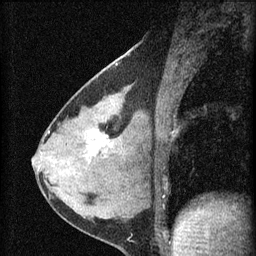
Breast MRI (dynamic contrast-enhanced), one sagittal slice; slice 28 of 60 in the series (ordered by position); dynamic contrast-enhanced series, image 2 of 4 at this slice position (ordered by acquisition); 1.5 T; TE 4.2 ms, TR 8.2 ms; 2 mm slice thickness; 256 × 256 image matrix, field of view 180 × 180 mm. Female patient, age 37 years.
Annotated regions visible in this slice (semi-automatic segmentation, software-assisted and operator-edited):
- analysis volume of interest (the breast-tissue region the enhancement analysis was run in; not a lesion): bounding box [x1, y1, x2, y2] px = [77, 116, 127, 175]
- tumour enhancement mask (voxels above the 70 % enhancement threshold inside the analysis volume of interest): [90, 135, 110, 154]